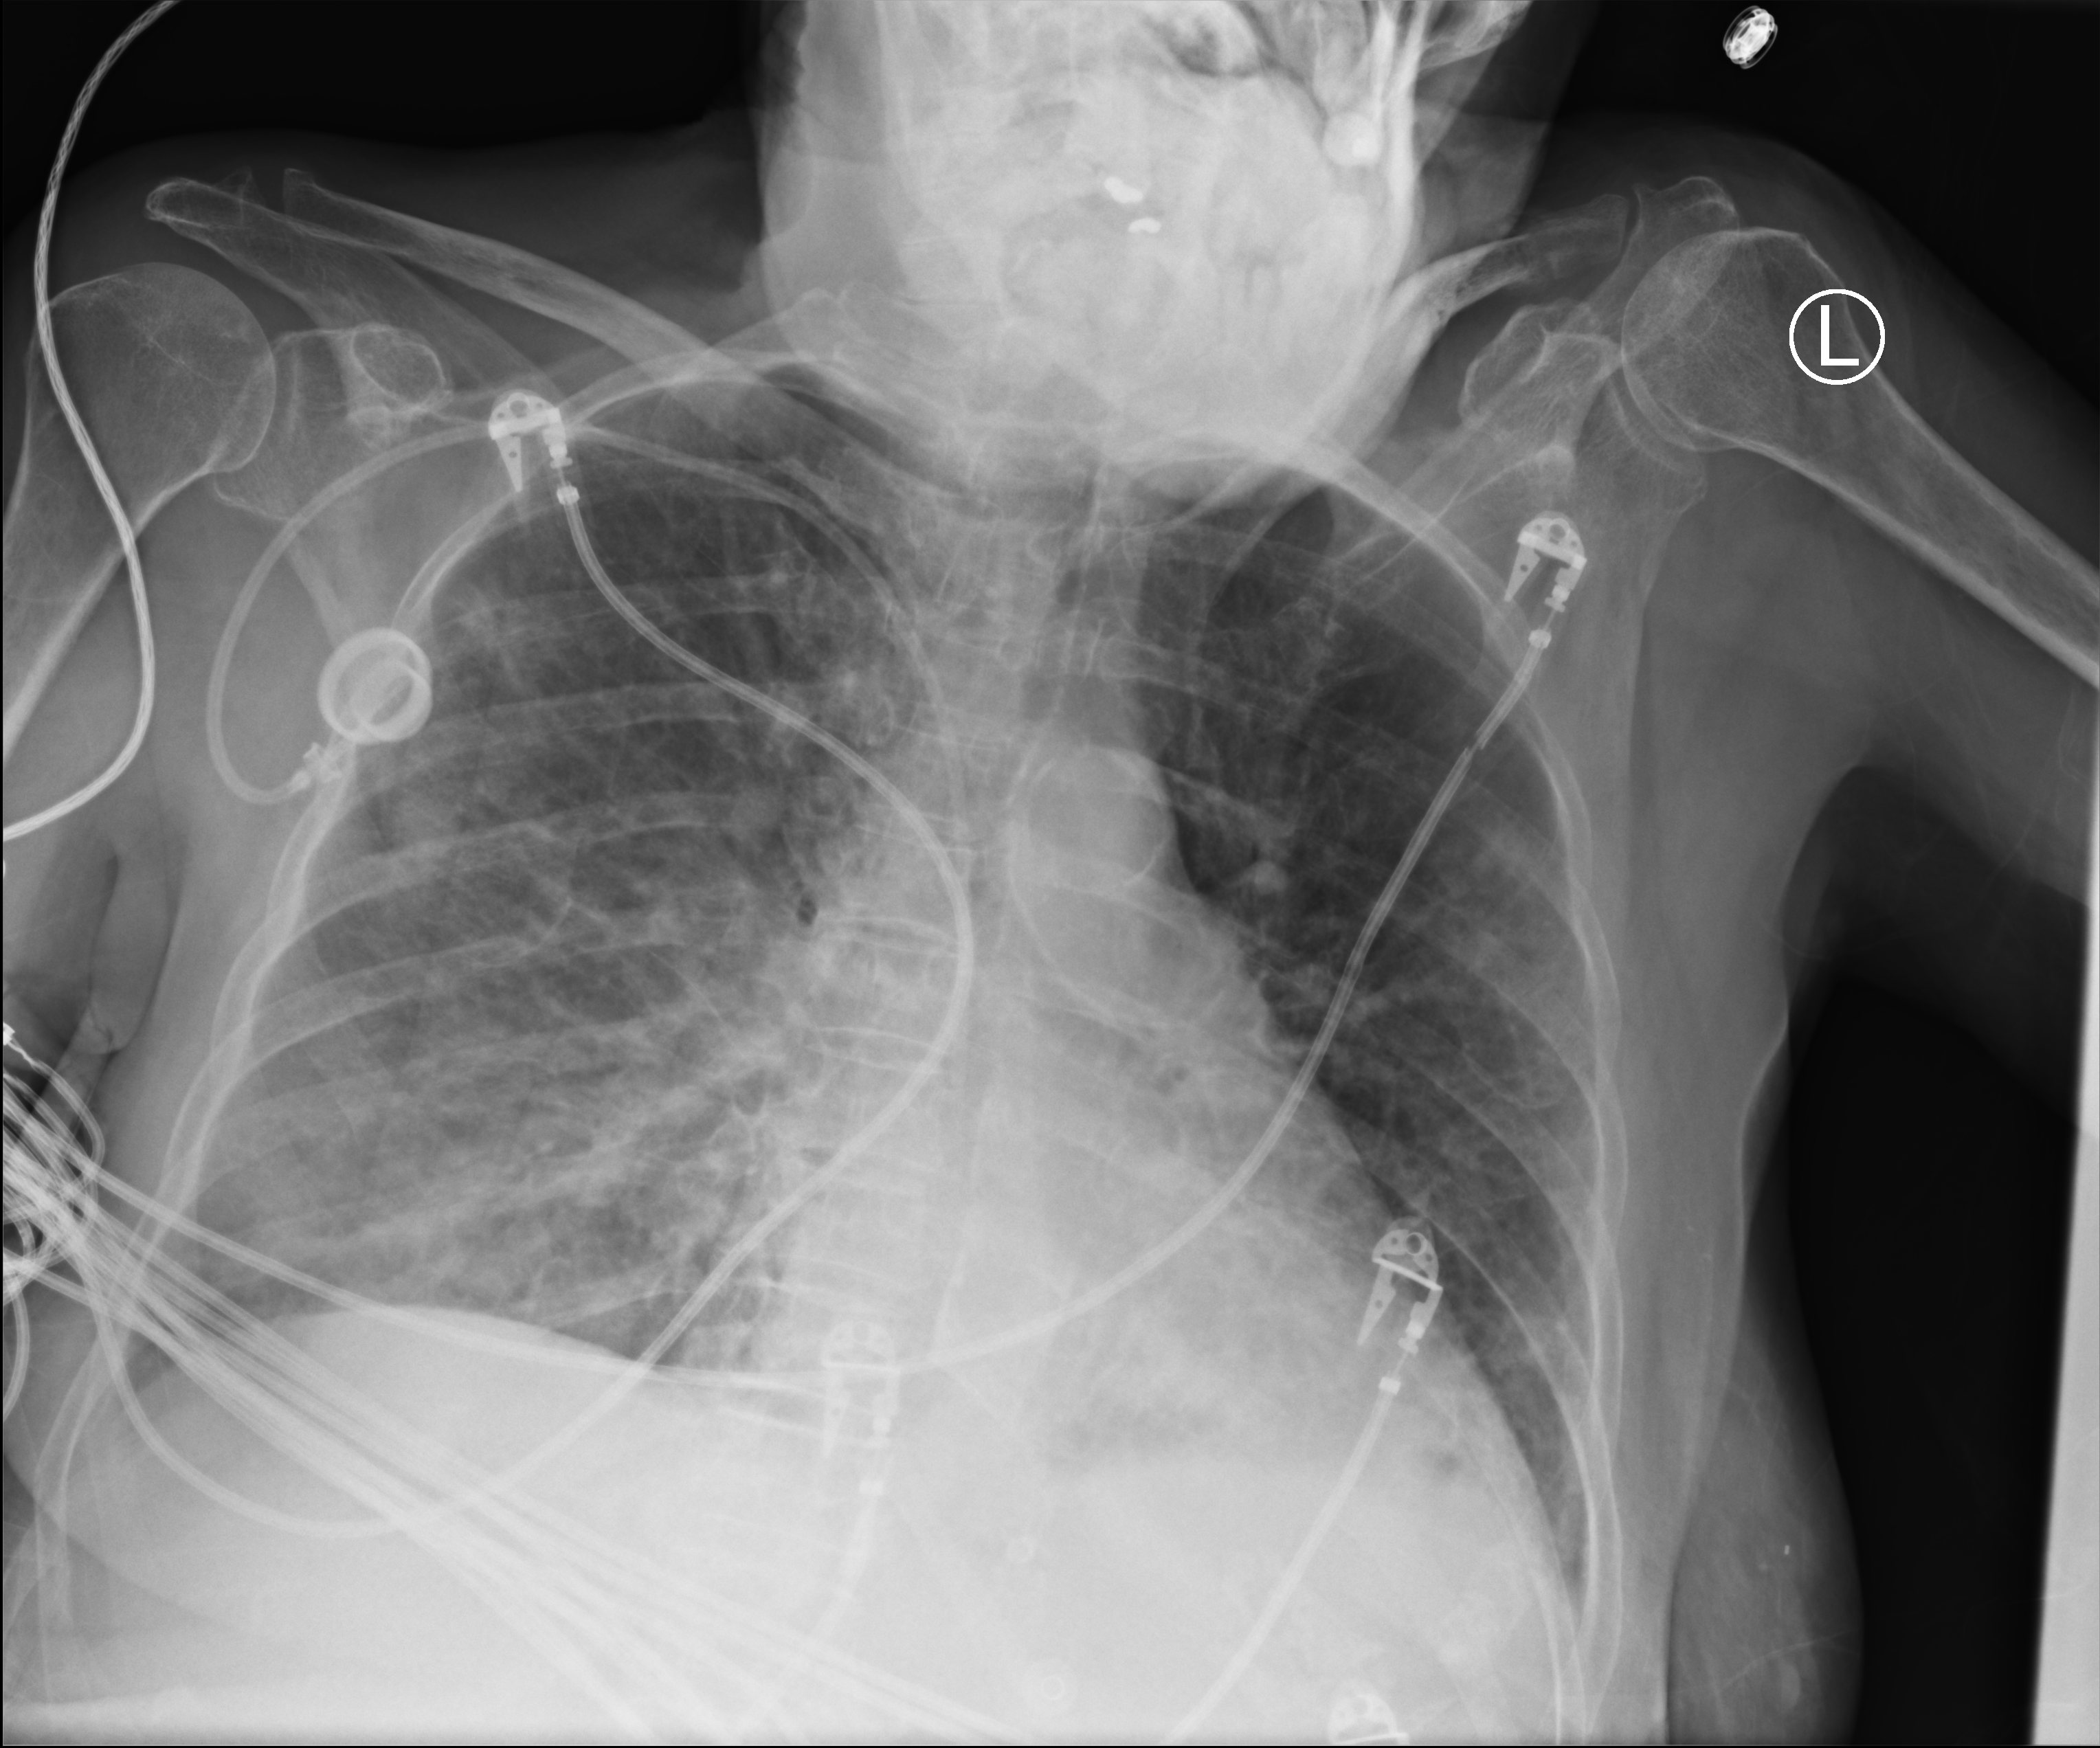
Portable chest radiograph, anteroposterior (AP) projection. Patient hospitalised with COVID-19; female, aged 75–90 years.
From the hospital-stay record, not from the radiograph (when in the stay this image was taken is not recorded): mechanically ventilated during this hospital stay: no.